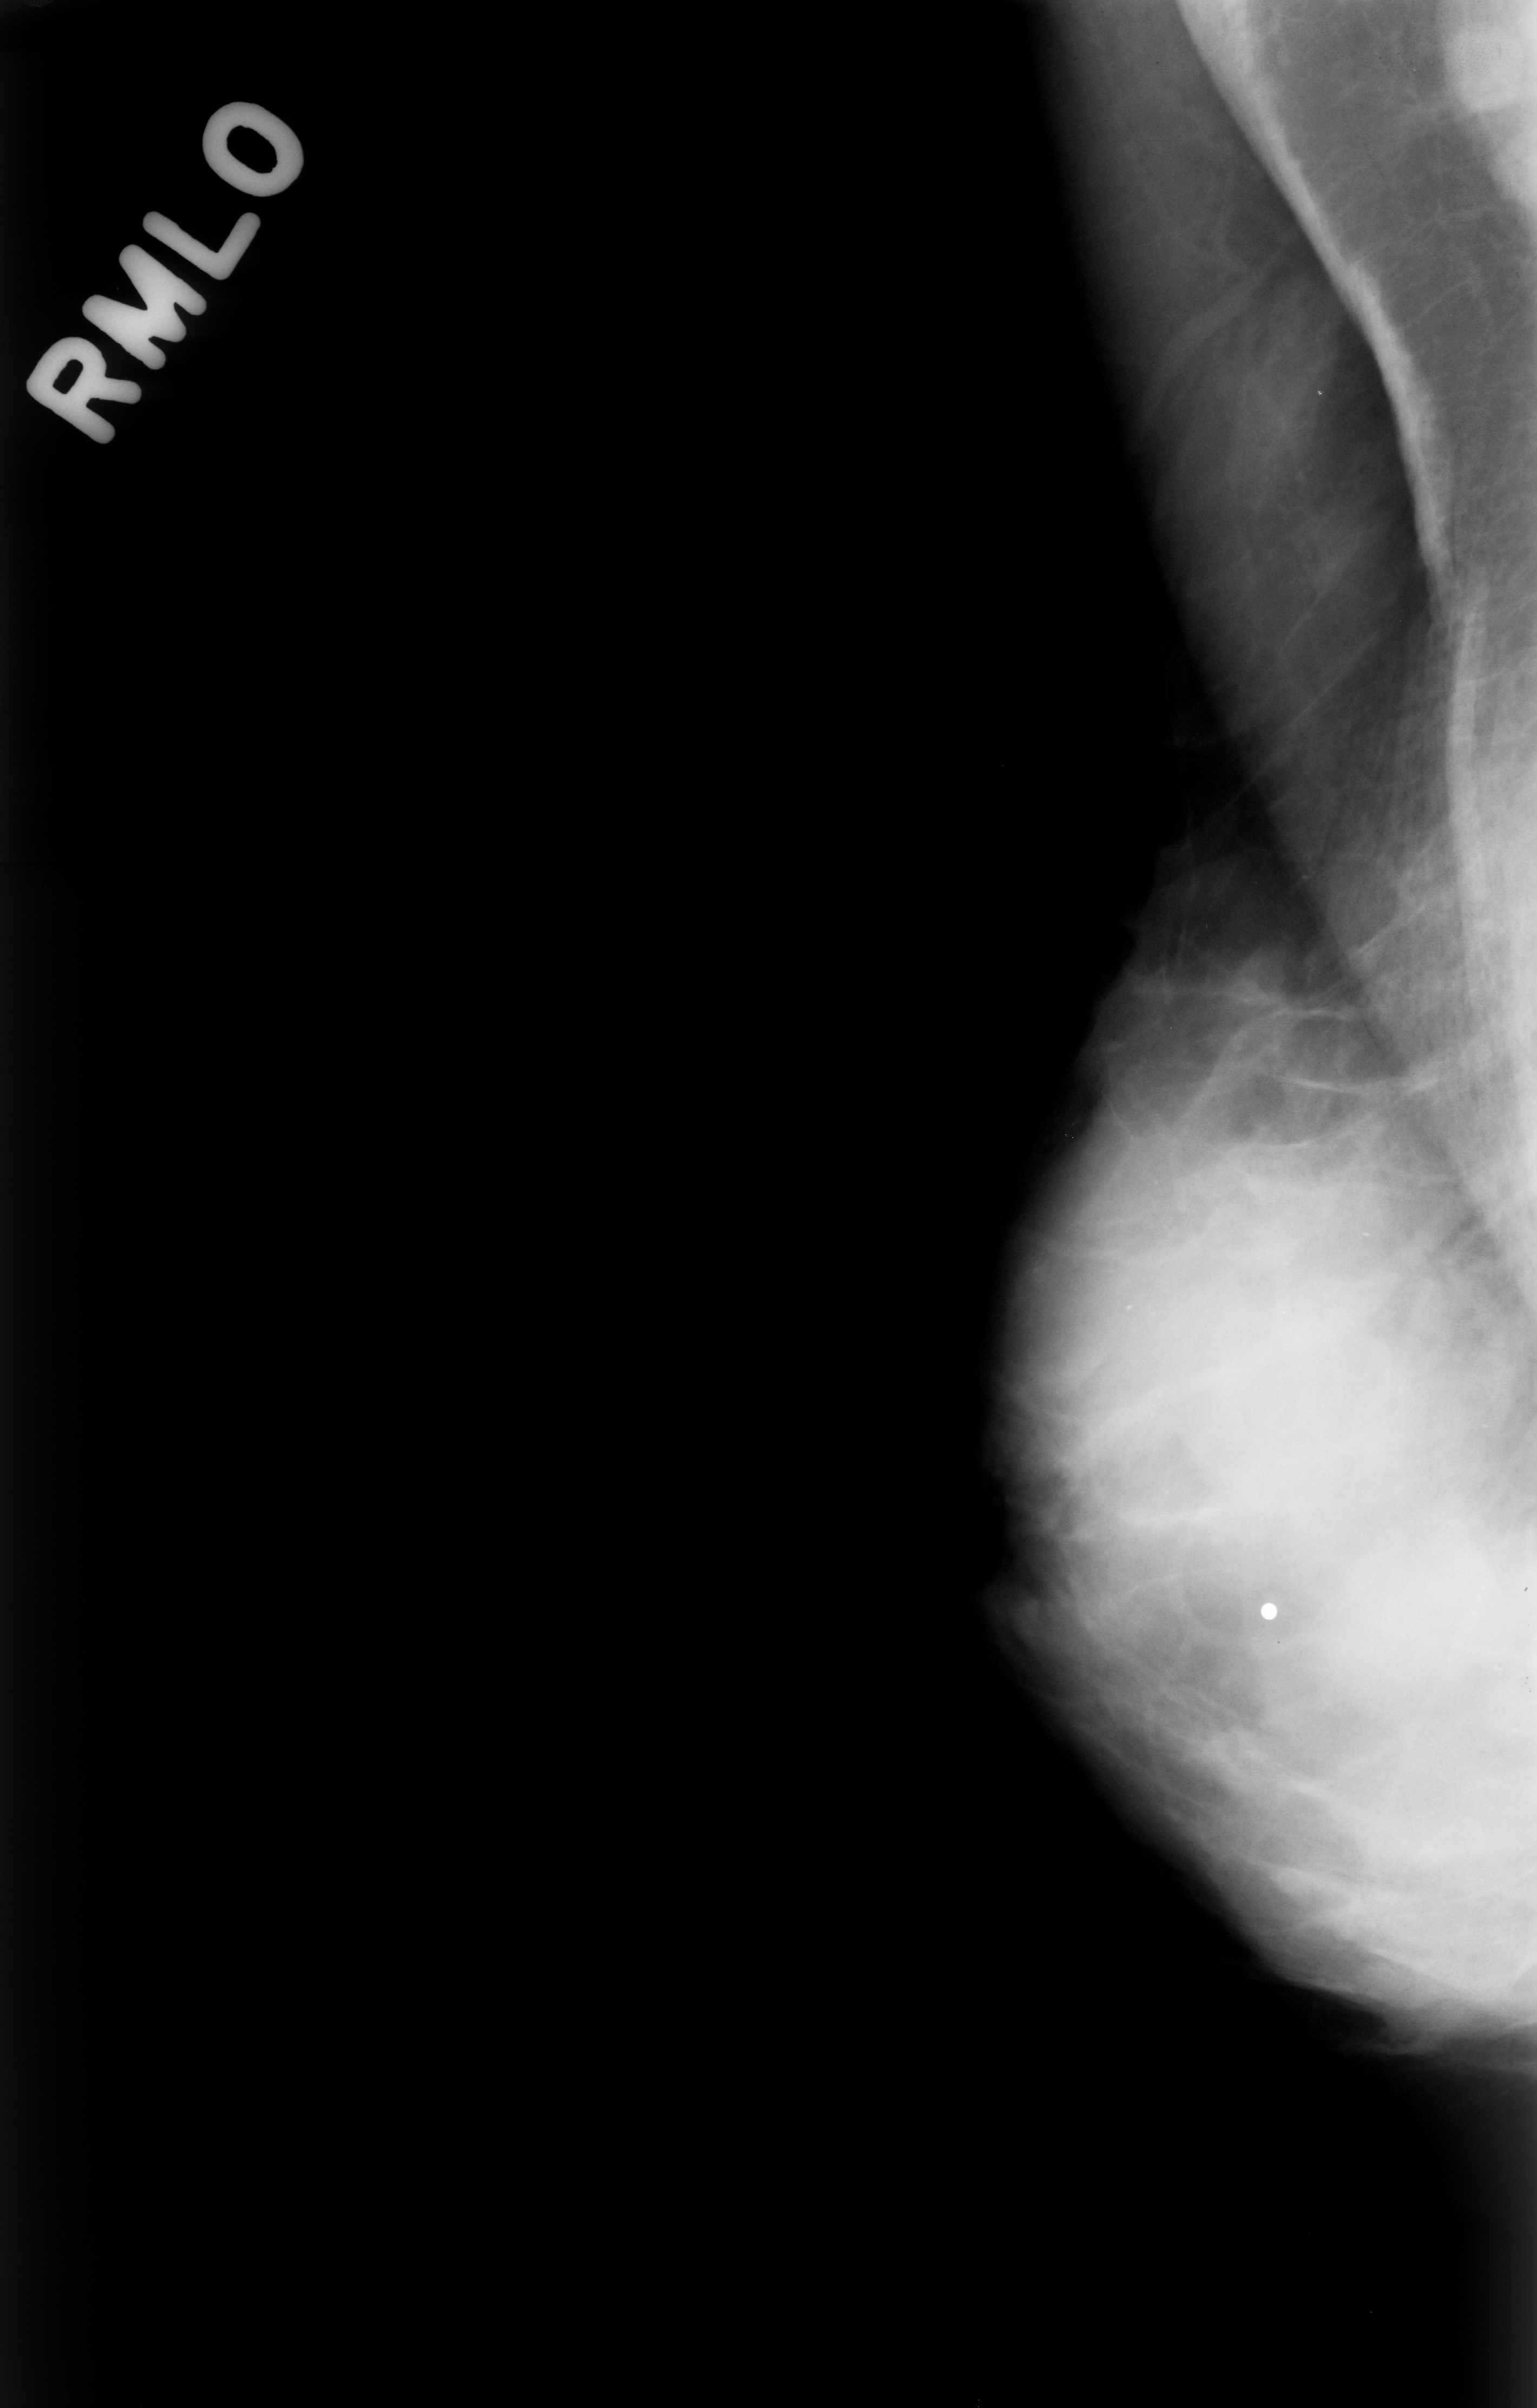
Digitized screen-film mammogram; right breast; mediolateral oblique (MLO) view; 1537 × 2408 image matrix.
Expert-marked regions of interest on this image (one box per marked abnormality):
- calcifications, morphology punctate, distribution diffusely scattered; BI-RADS assessment category 2; subtlety rating 4 on a 1 (subtle) to 5 (obvious) scale; pathology (as recorded): benign: bounding box (x1, y1, x2, y2) in pixels: (1078, 1095, 1529, 1859)